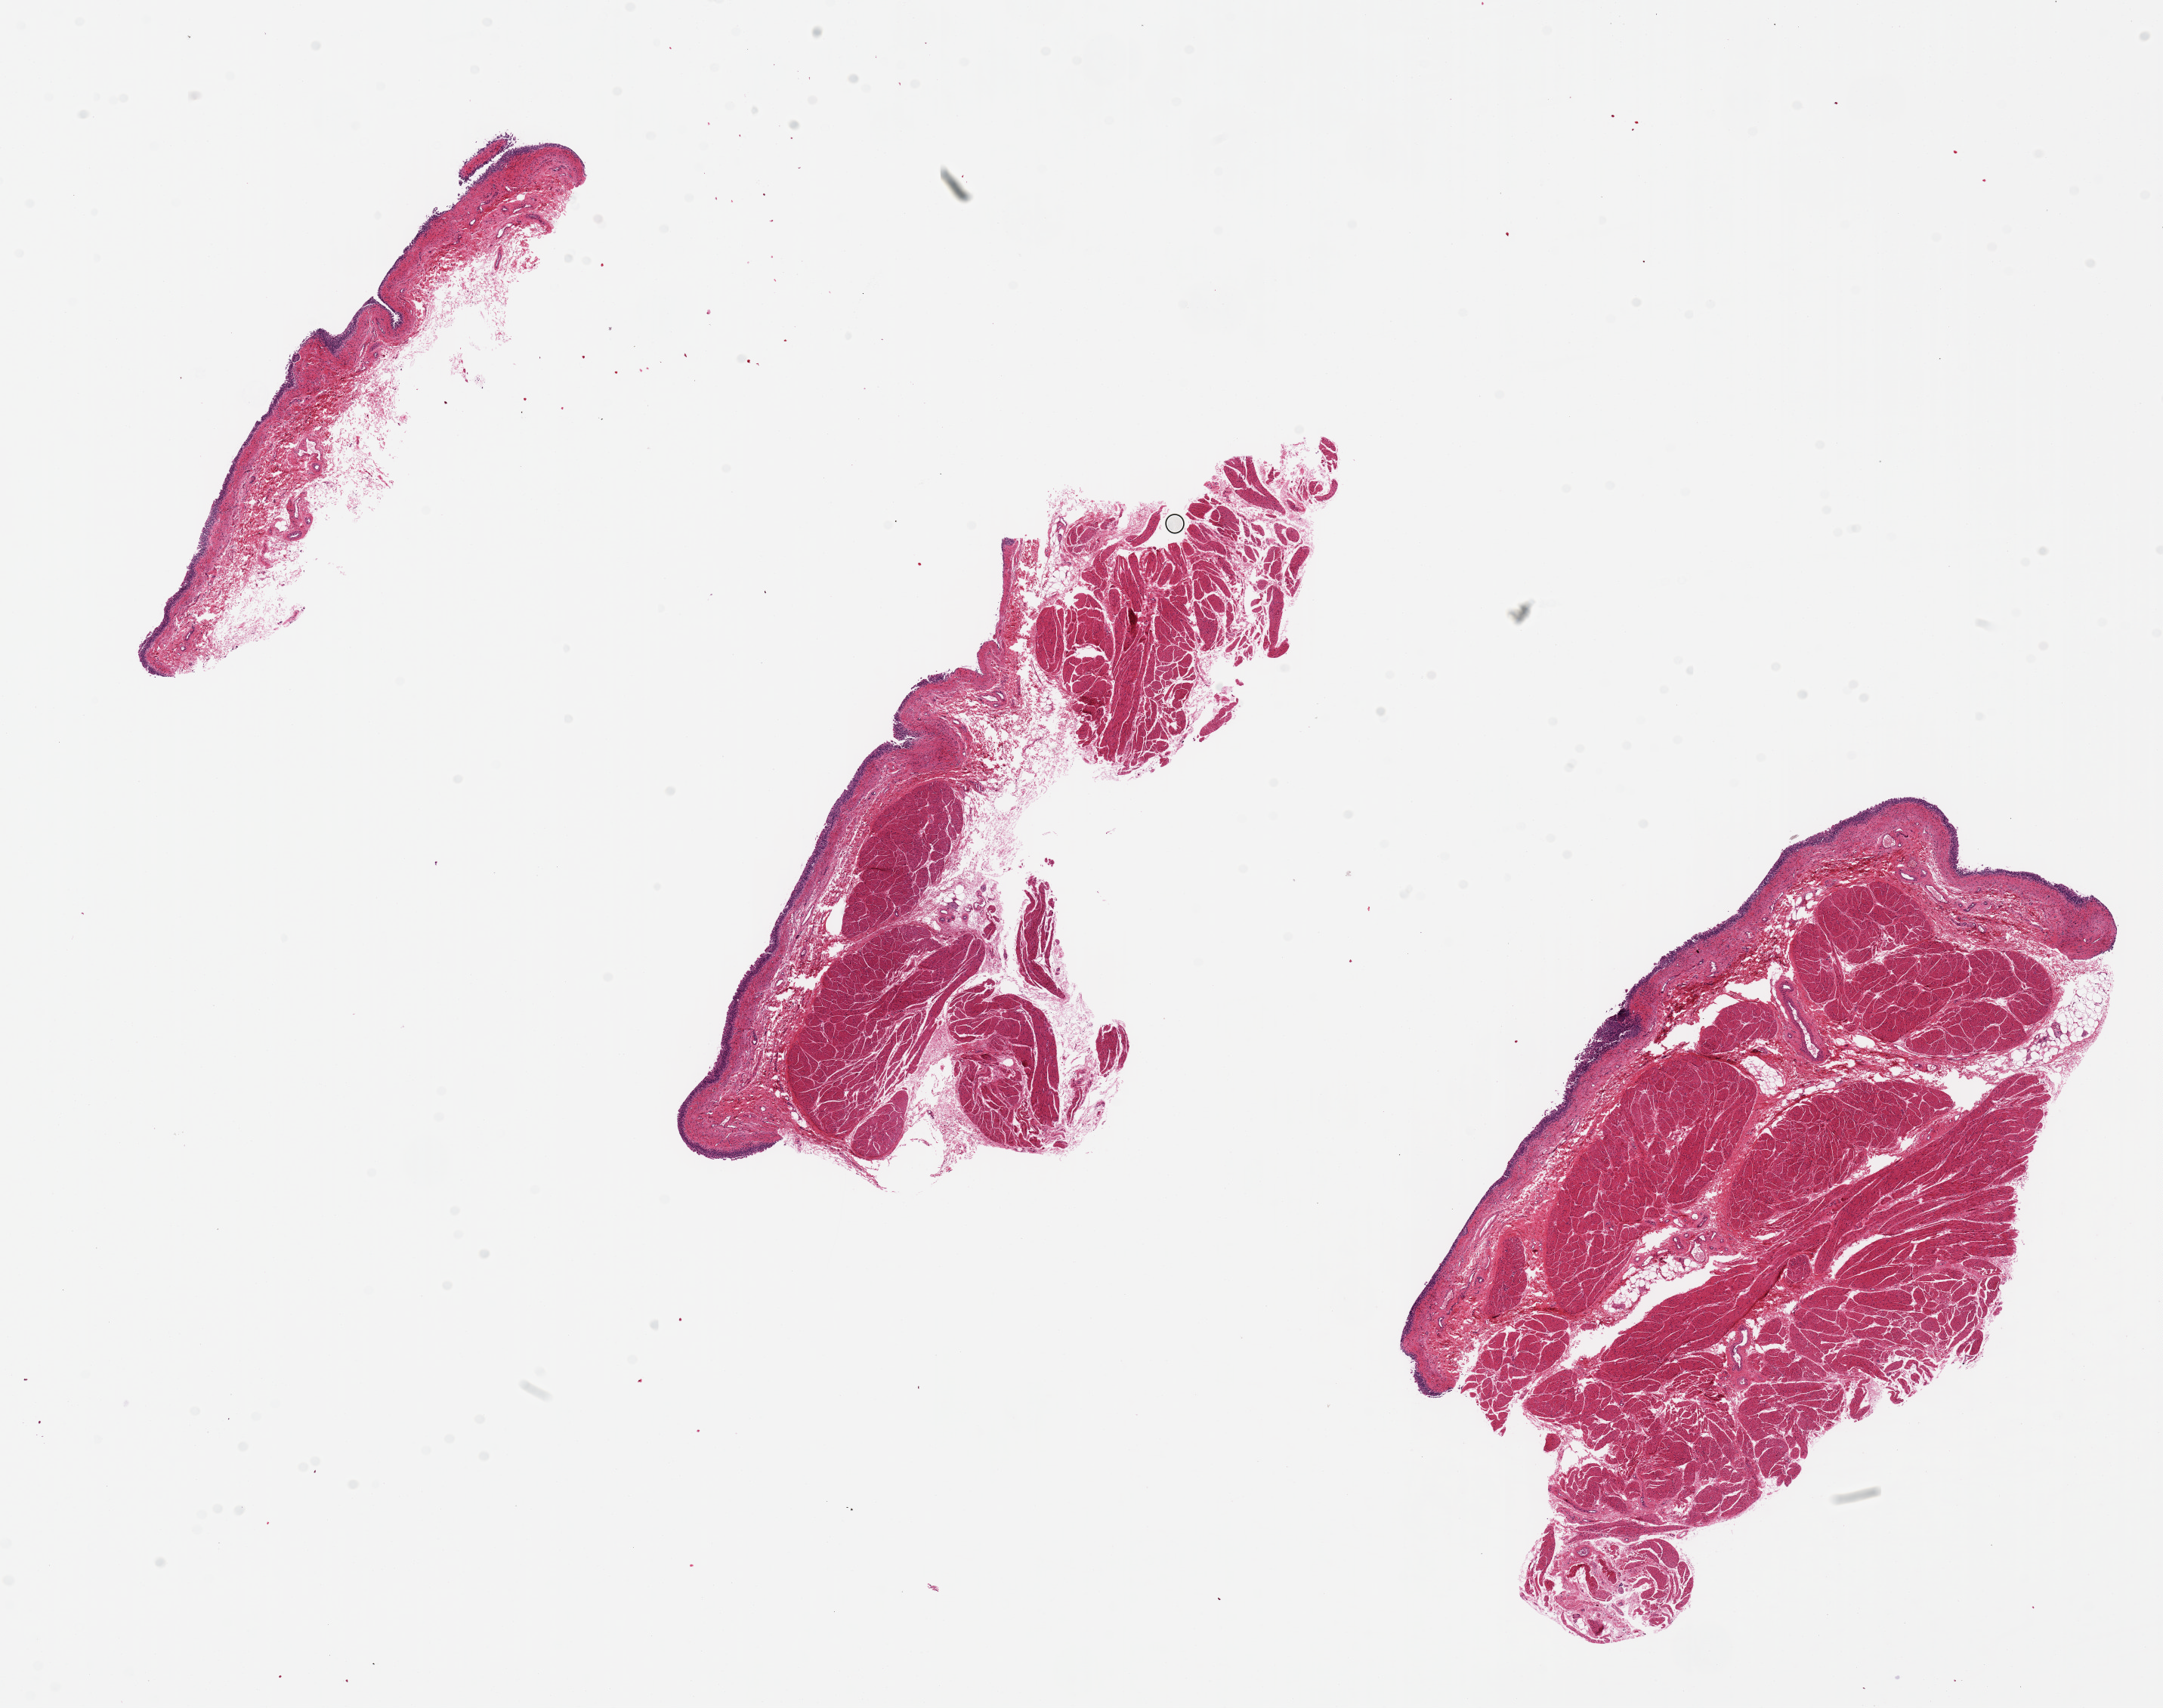
H&E whole-slide image, whole scanned area (about 22.6 x 17.9 mm, acquisition: 20x scan) shown as a low-resolution overview; PAXgene-fixed, paraffin-embedded tissue; section of urinary bladder (target tissue); tissue donor sample.
• review note (as recorded): mucosa is ~ 1.5% of specimen thickness